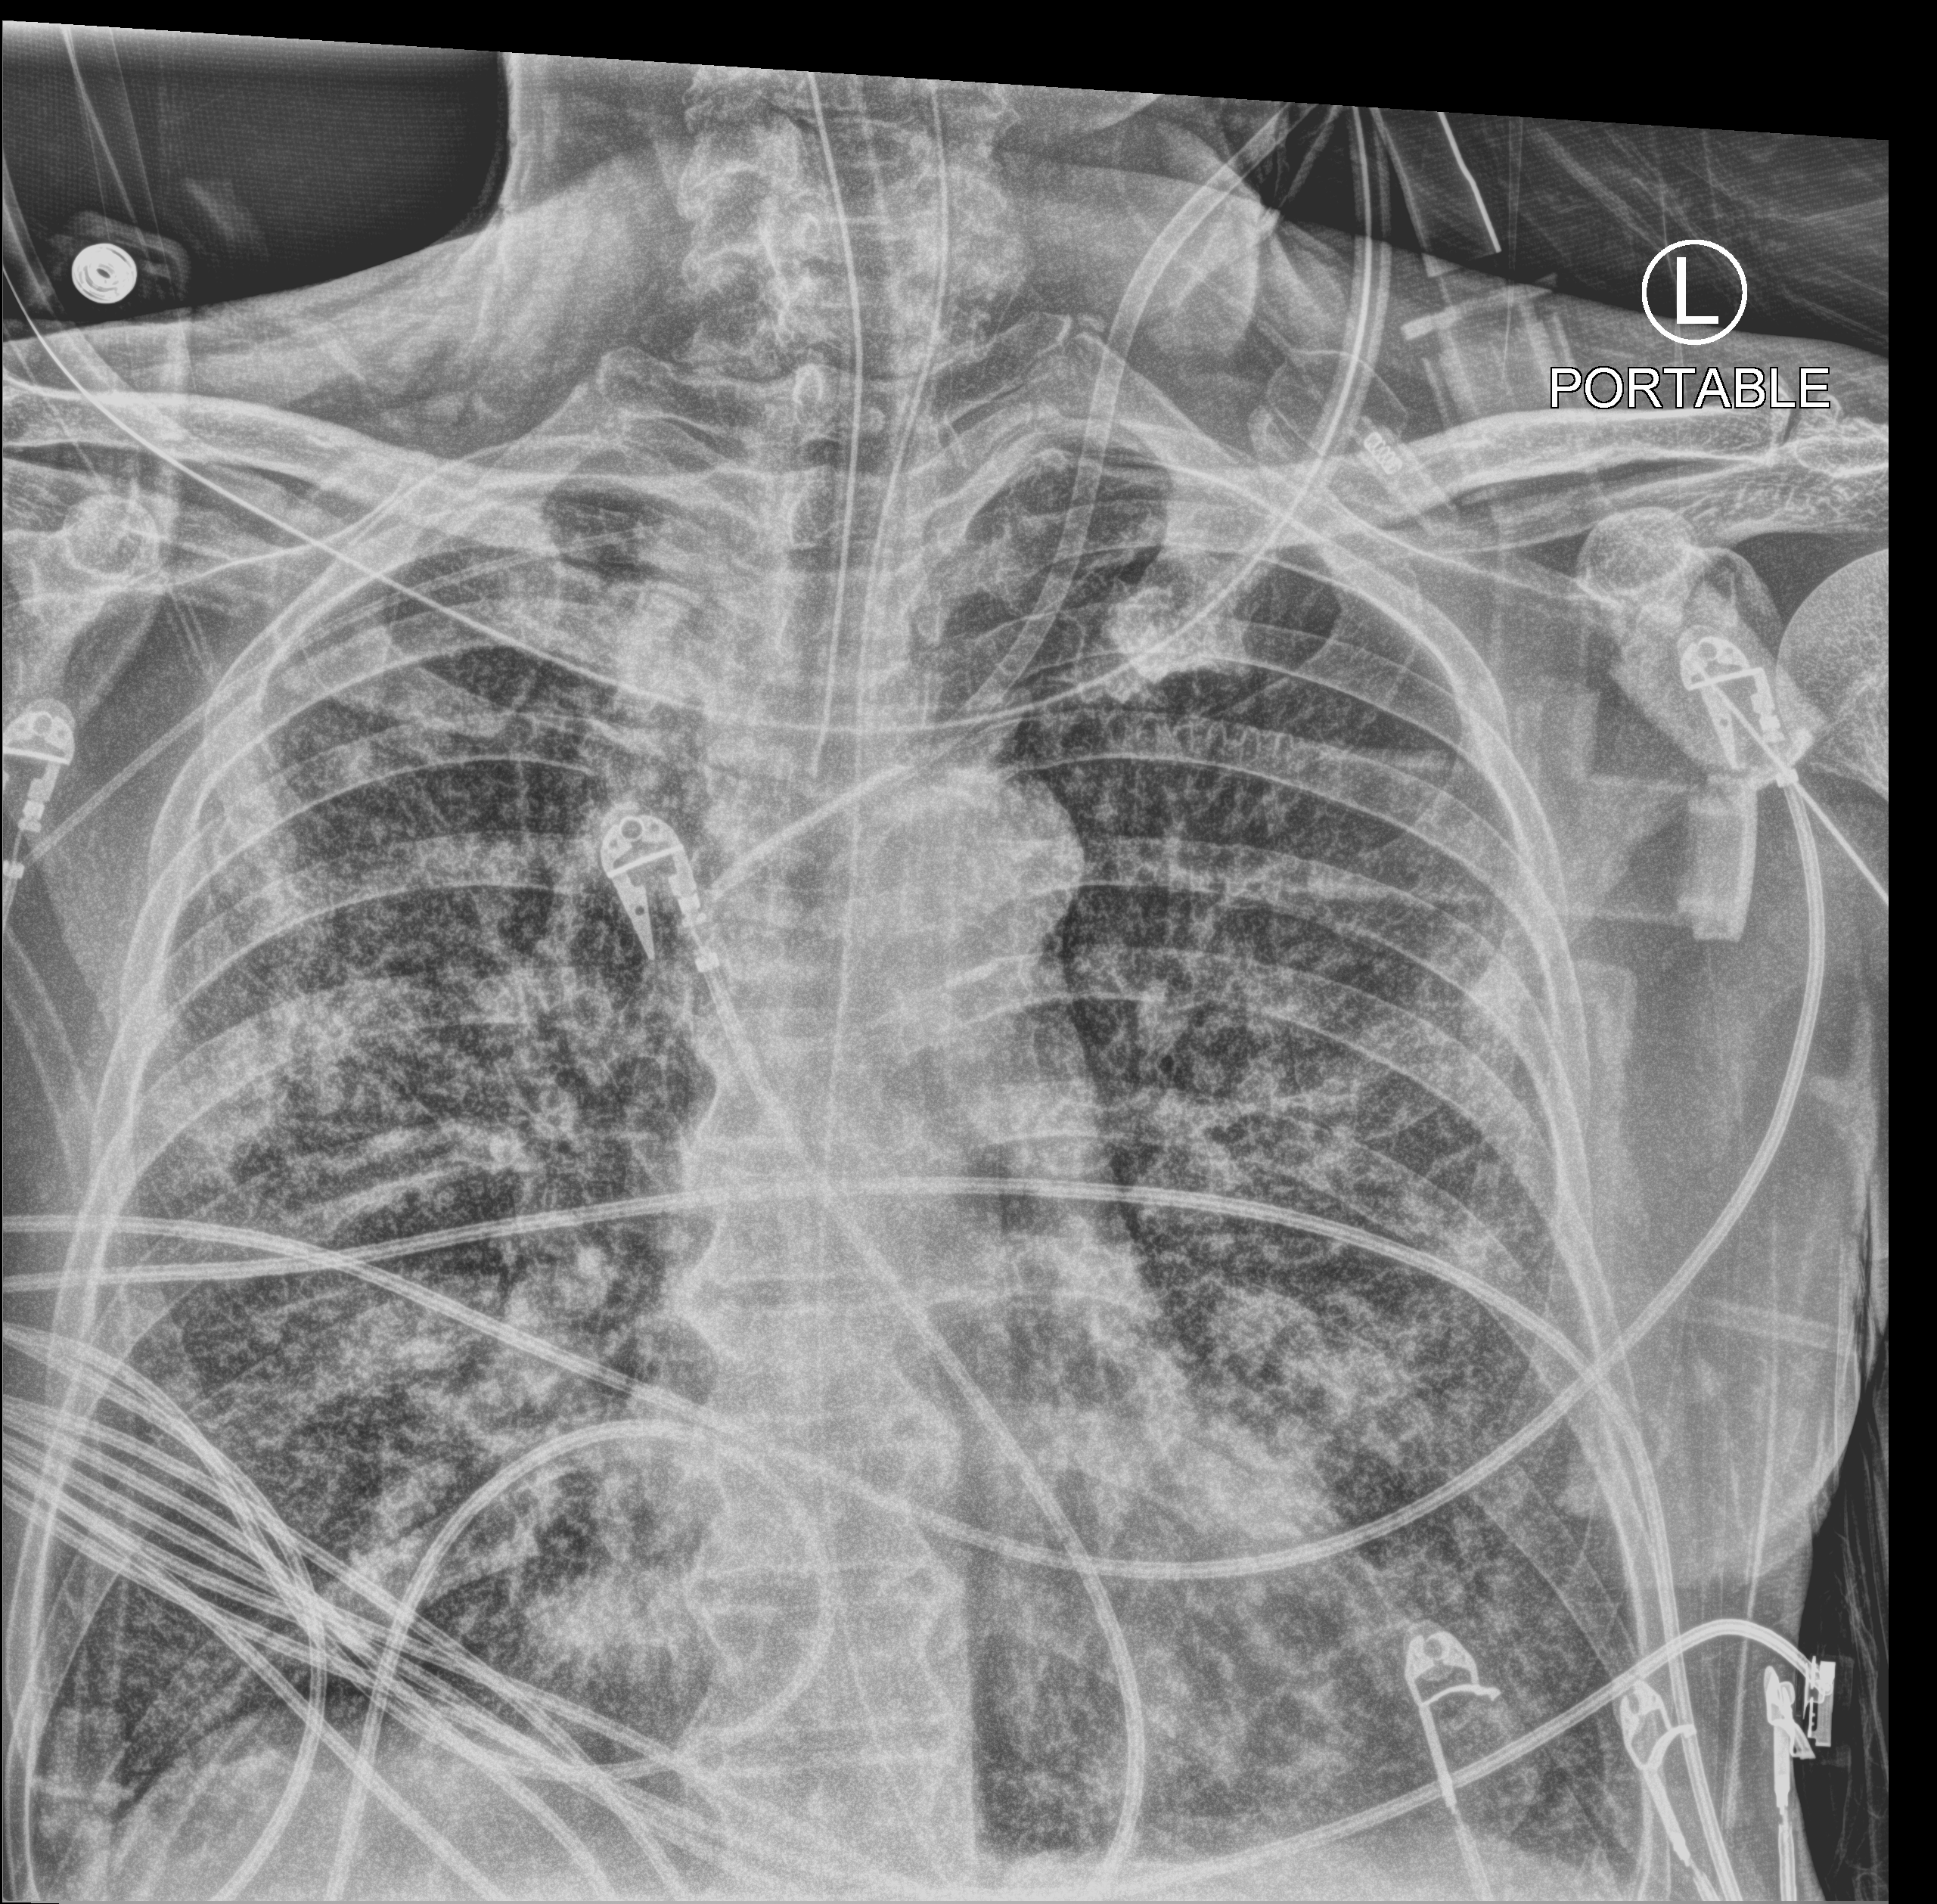
Portable chest radiograph; anteroposterior (AP) projection. Male patient hospitalised with COVID-19, age 60–74 years.
From the hospital-stay record, not from the radiograph (when in the stay this image was taken is not recorded): mechanically ventilated during this hospital stay: yes; COPD (admission record): no.